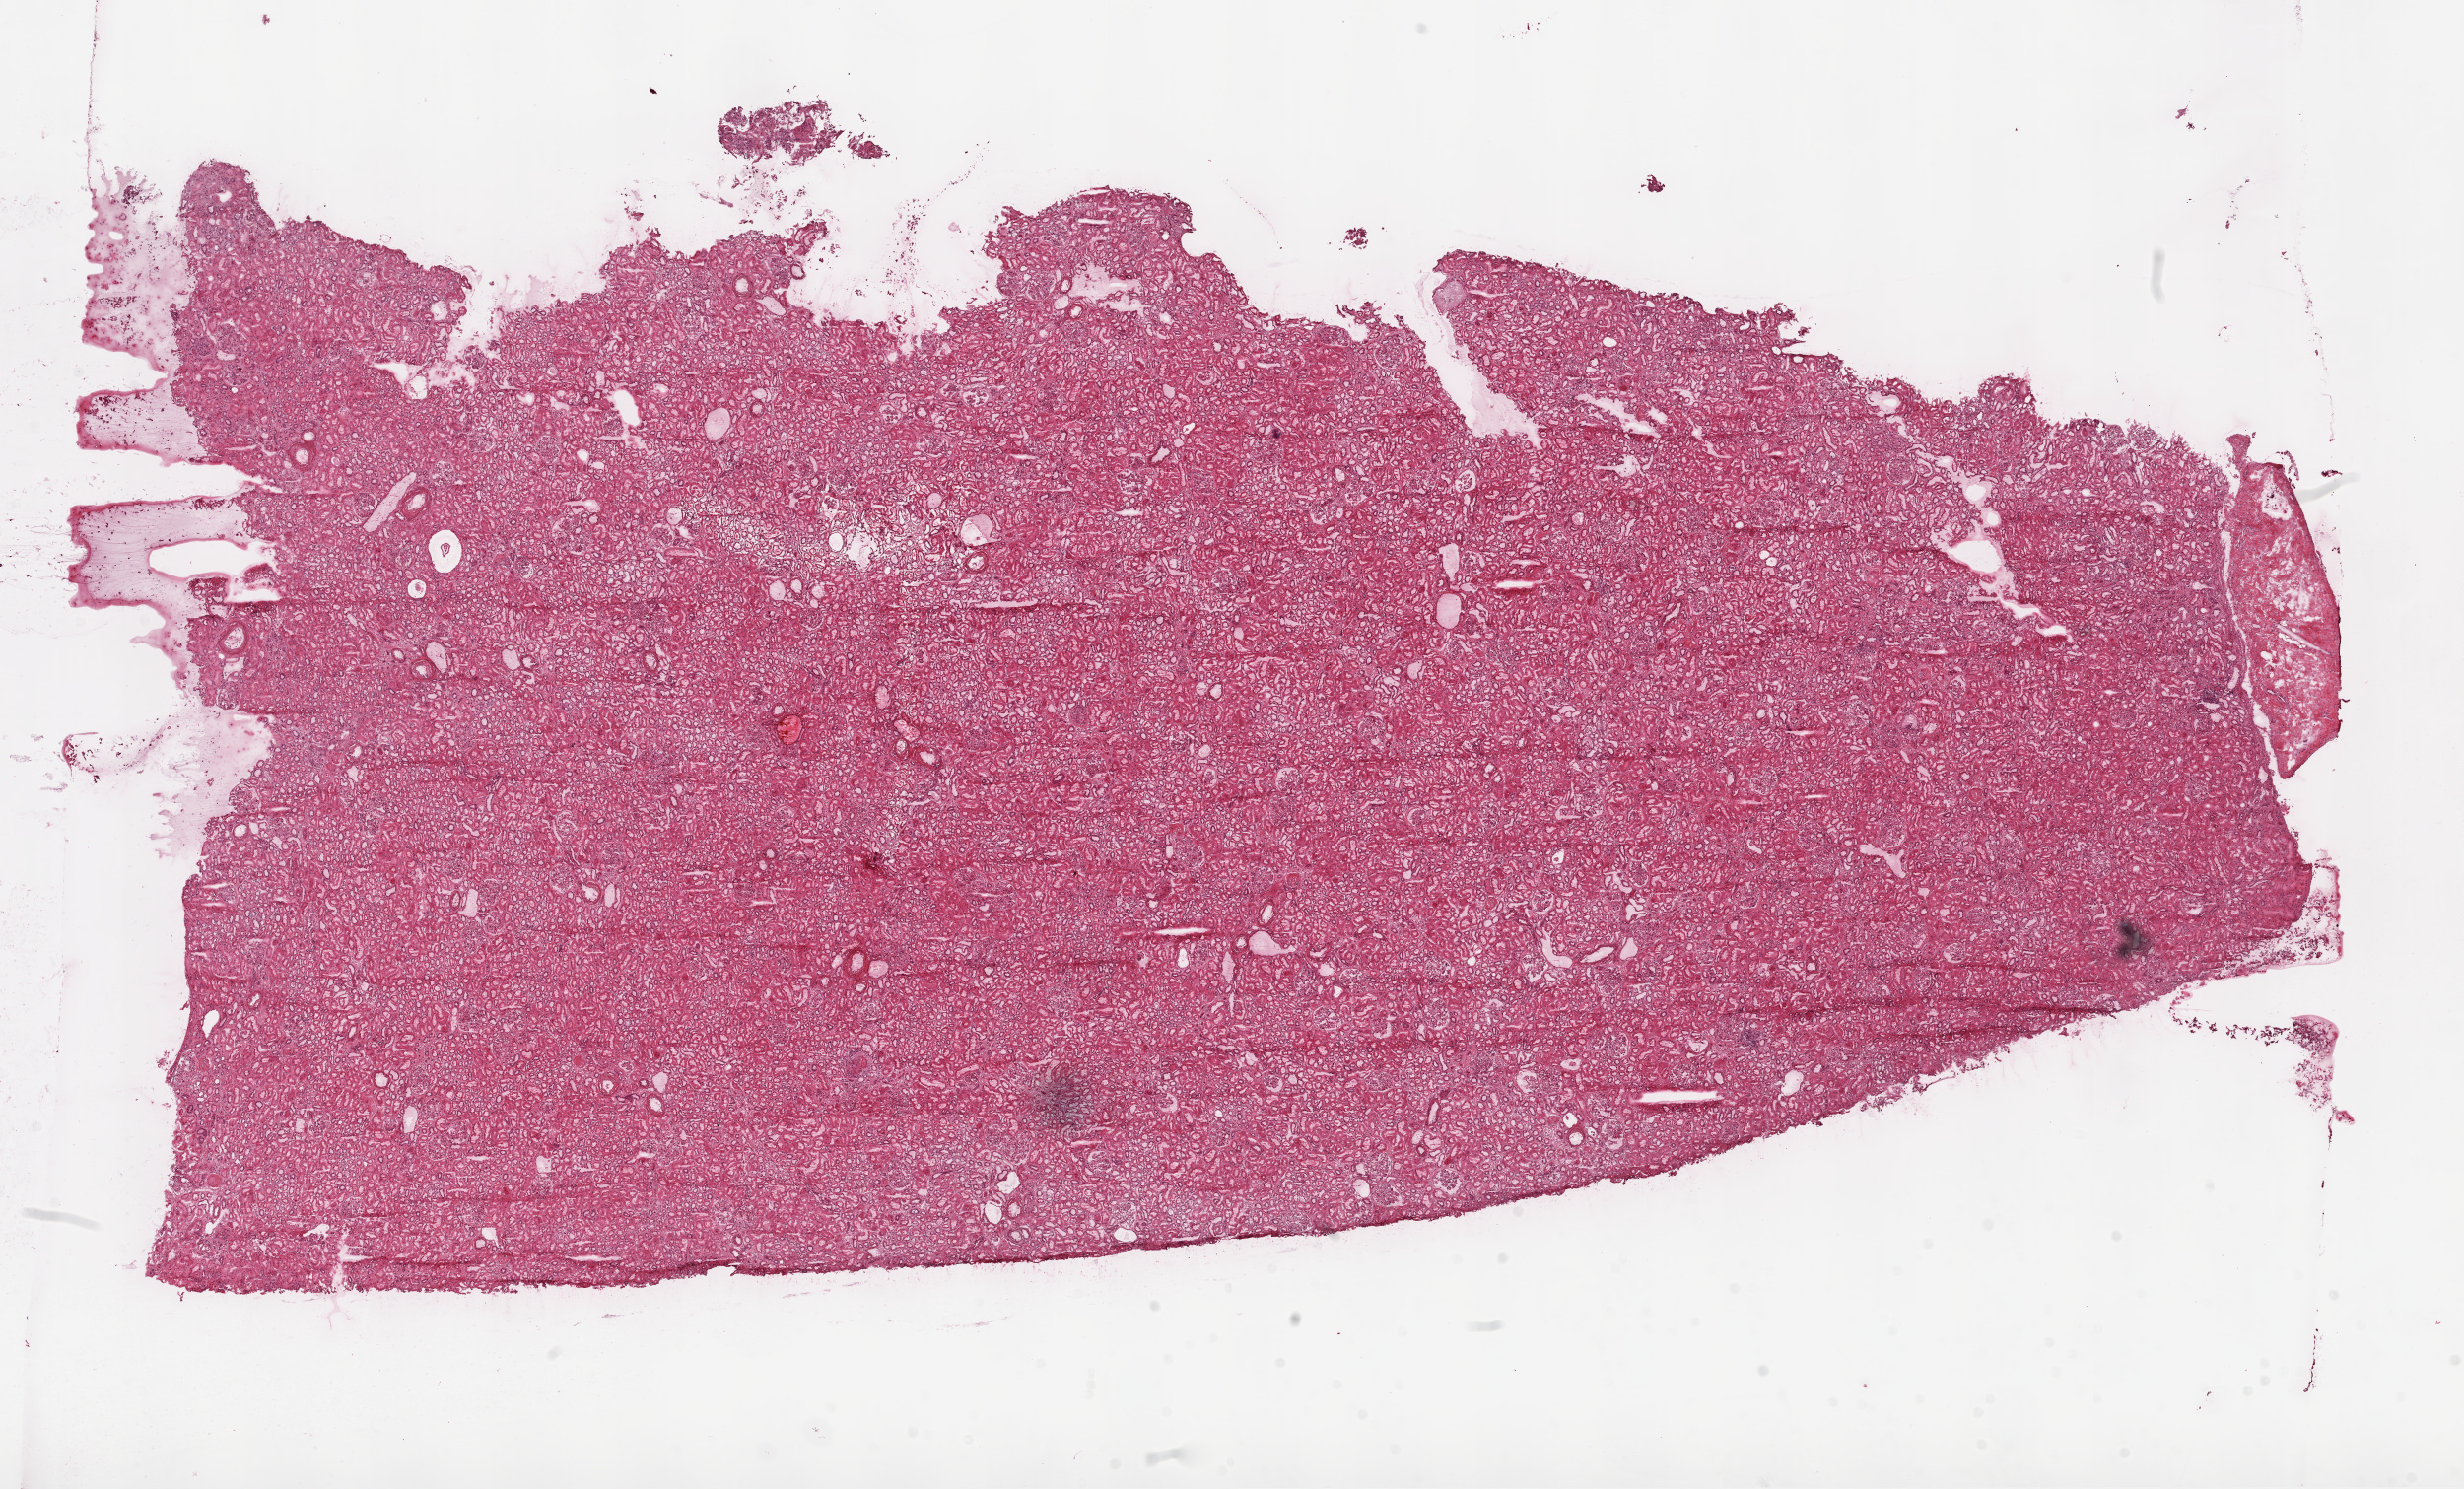
Digitized H&E tissue section (whole slide), low-resolution overview of the scanned area, about 20.1 x 12.1 mm (slide scanned at 20x); frozen section; solid tissue normal (non-tumour tissue) sample from the kidney. Female patient; age at initial diagnosis 76 years.
This section: solid tissue normal sample (biorepository sample class). Patient diagnosis: Clear cell adenocarcinoma, NOS.